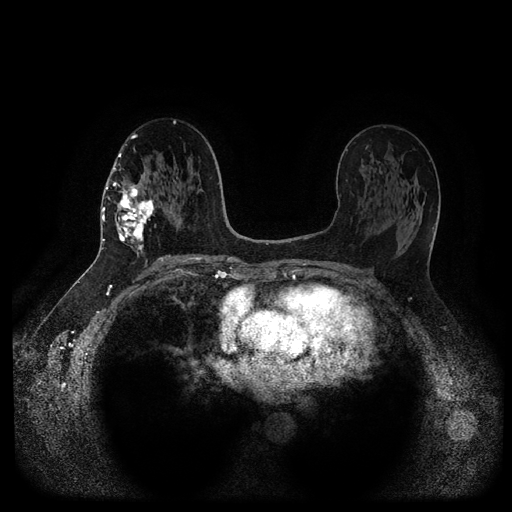
Breast MRI (dynamic contrast-enhanced, multi-phase), one axial slice. Position 57 of 116 along the scan axis. Dynamic contrast-enhanced series, time point 2 of 5 at this slice position (early post-contrast). 1.5 T. TE 2.6 ms, TR 5.3 ms. 2 mm slice thickness. 512 × 512 image matrix, field of view 360 × 360 mm. Female patient, age 58 years.
Outlined on this slice (semi-automatically segmented with operator editing):
- breast lesion (labelled 'tumour' in the annotation; benign lesions carry a separate 'benign' label): box from (x=111, y=175) to (x=156, y=262) px